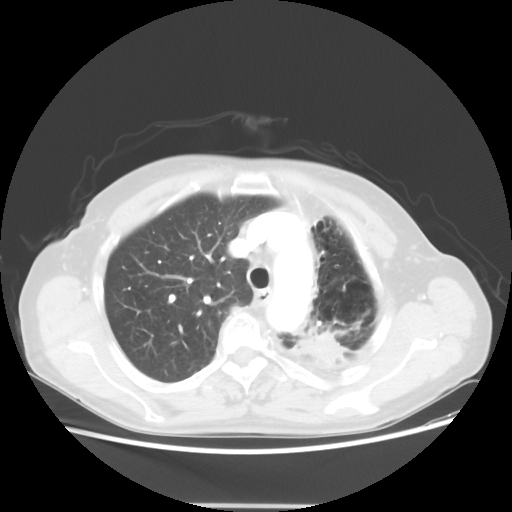
Chest CT, one axial slice; position 40 of 56 along the scan axis; reconstruction kernel STANDARD; lung window (W 1500 / L -600 HU); 5 mm slice thickness; 512 × 512 image matrix, field of view 377 × 377 mm. Female patient, age 63 years. From the clinical record (not read from this slice): clinical TNM (as recorded): T2a N0 M0.
Structures marked on this image (bounding box drawn by a radiologist):
- lung tumour (recorded histology: adenocarcinoma): bounding box <298,323,346,371> (left, top, right, bottom; pixels)